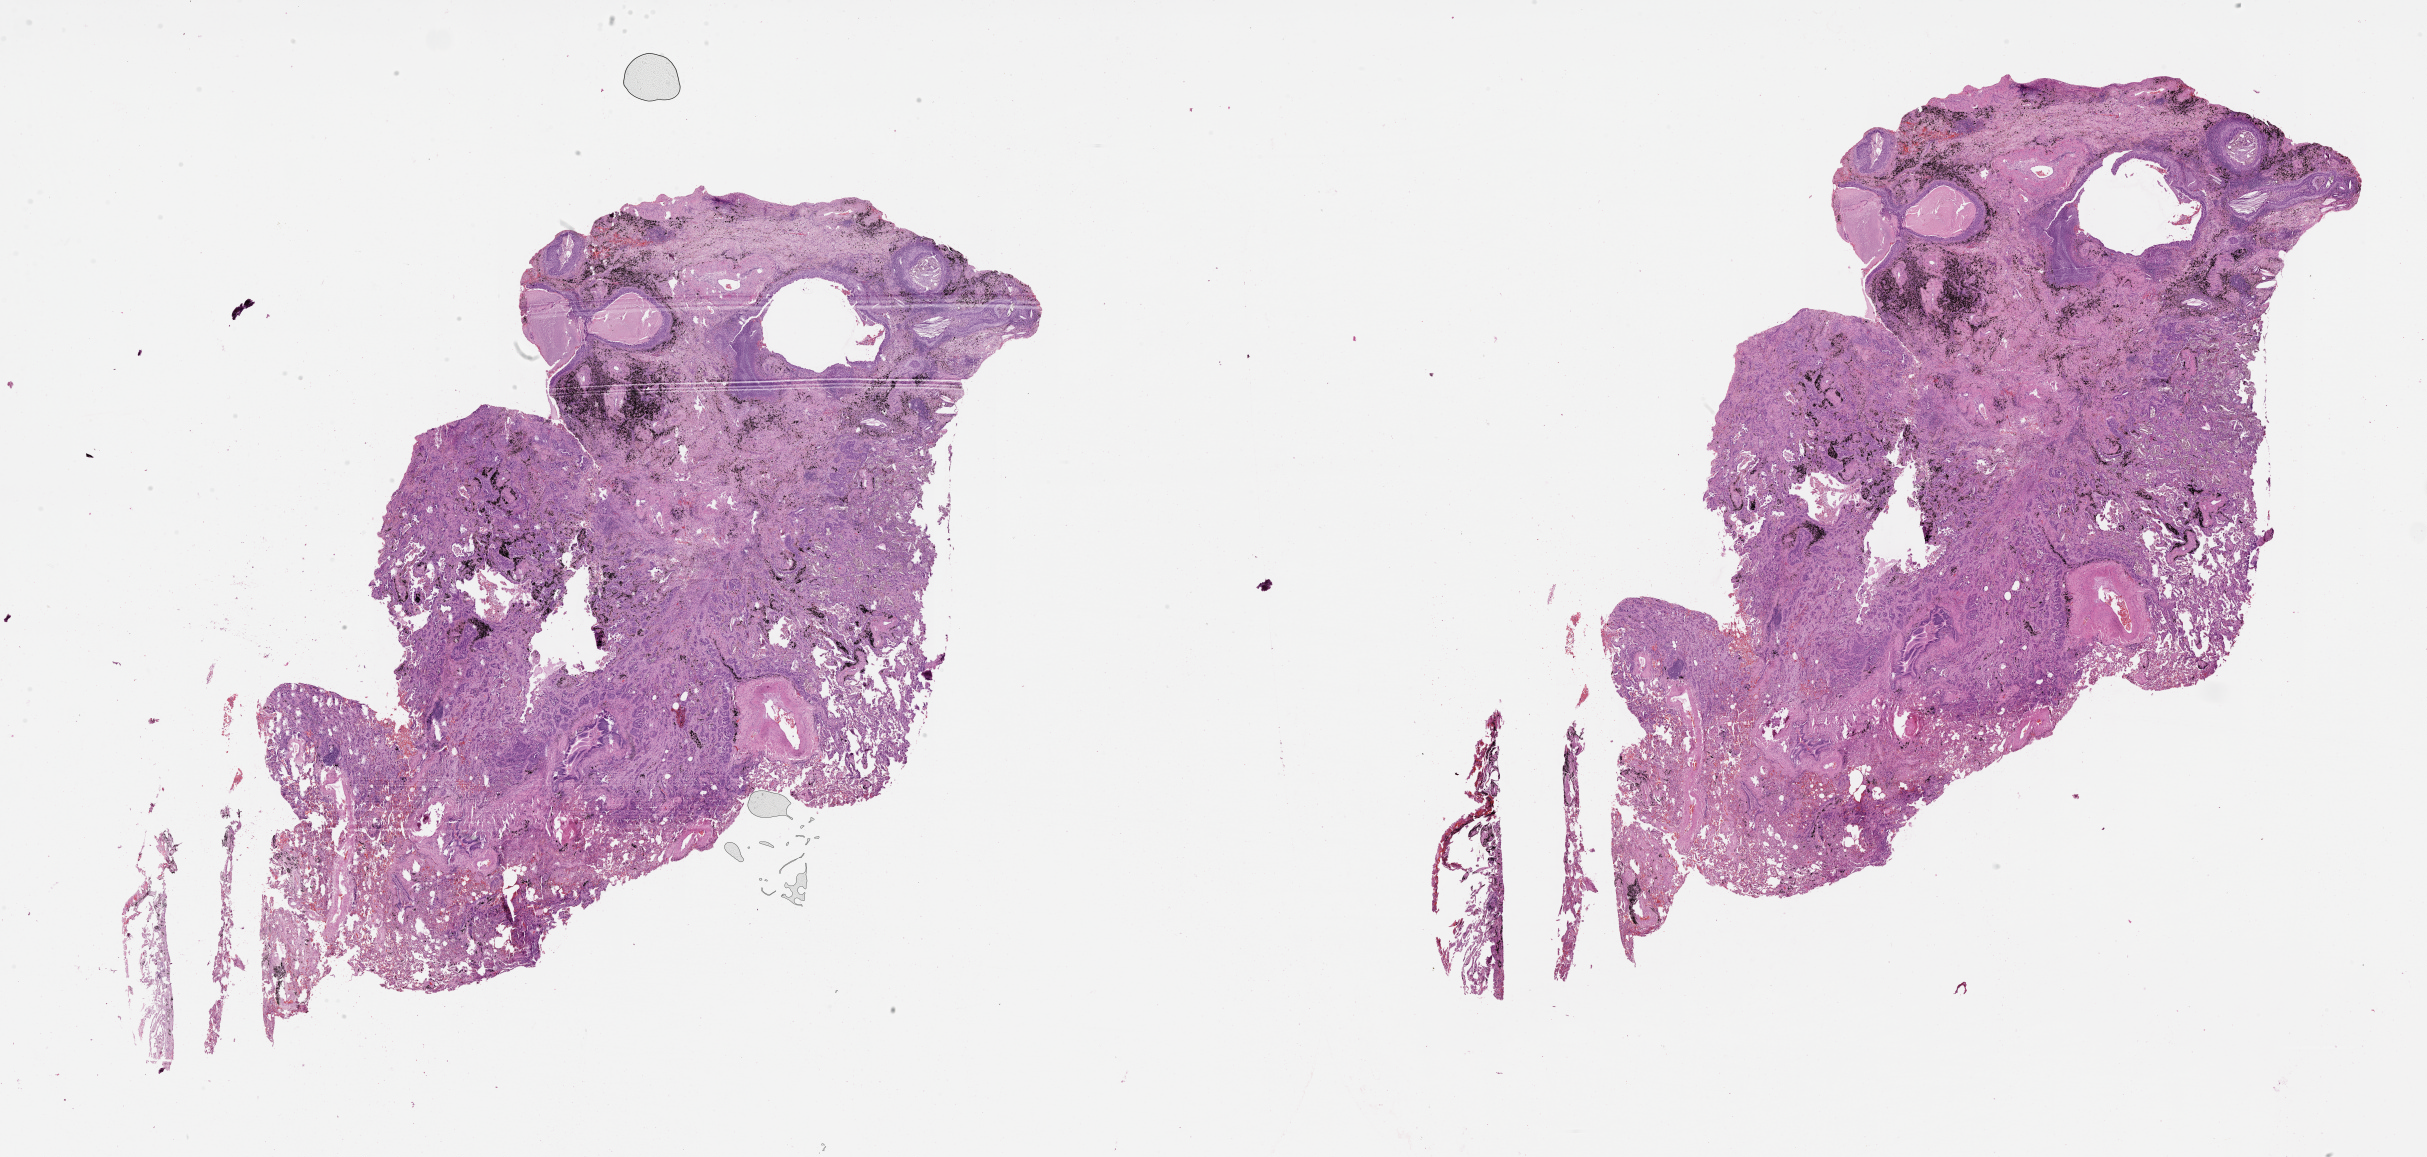
Whole-slide histology image, H&E-stained — low-resolution overview of the scanned area, about 39.1 x 18.6 mm; lung, tissue type not recorded.
- patient diagnosis (cohort enrolment): squamous cell carcinoma (lung)